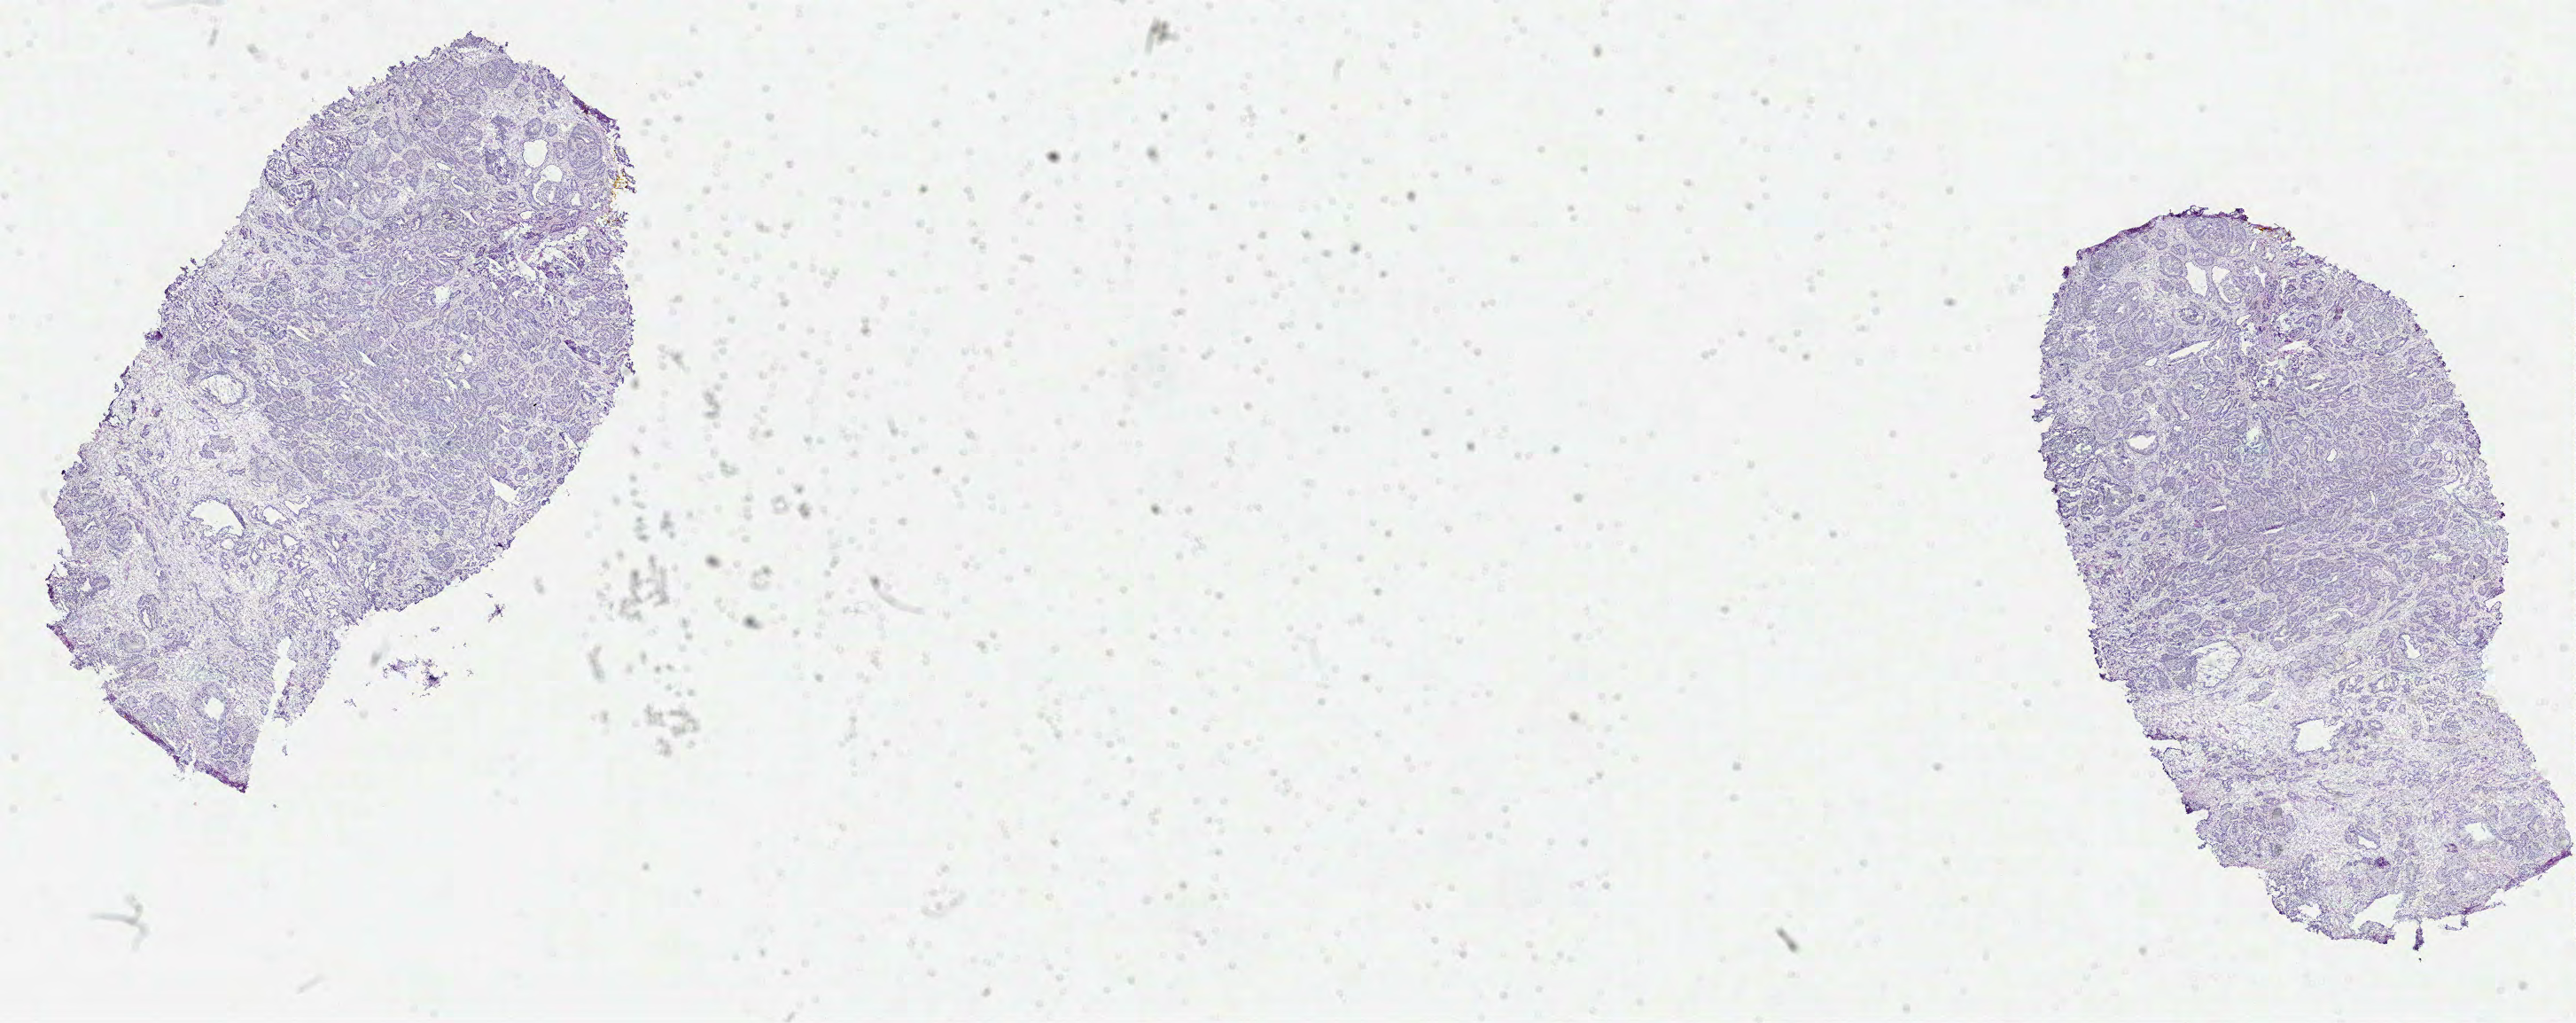
H&E whole-slide image, low-resolution overview of the scanned area, about 23.4 x 9.3 mm (slide scanned at 40x); formalin-fixed paraffin-embedded (FFPE) diagnostic section; prostate, primary tumour sample. Male patient; age at initial diagnosis 55 years. Gleason score: 7 (4+3).
• lymph nodes positive (case pathology): 1 of 4 examined
• pathologic diagnosis: Acinar cell carcinoma (prostate gland)
• laterality: bilateral